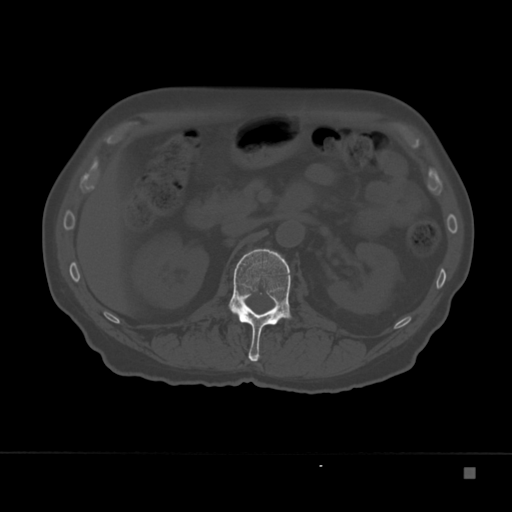
CT including the spine, one axial slice; position 109 of 332 along the scan axis; reconstruction kernel Br40s; 120 kVp; bone window (W 1800 / L 400 HU); 1.5 mm slice thickness; 512 × 512 image matrix. Male patient, age 72 years. Case-level facts recorded for this patient, not image findings: primary cancer: skeletal.
Structures marked on this image (semi-automatically segmented with operator editing):
- L1 vertebra: bounding box (x1, y1, x2, y2) in pixels: (228, 249, 292, 362)